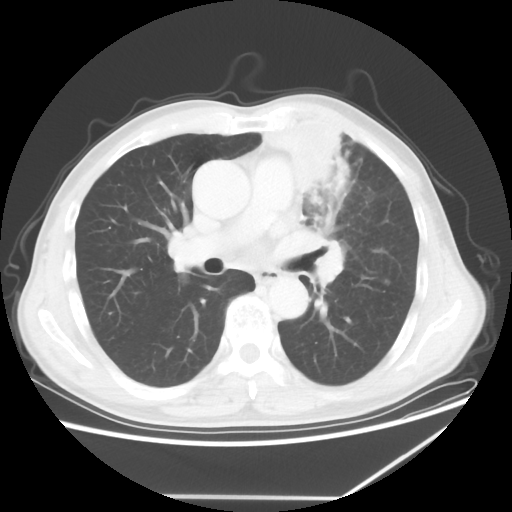
Chest CT, one axial slice; slice 35 of 64 in the series (ordered by position); lung window (W 1500 / L -600 HU); 5 mm slice thickness; 512 × 512 image matrix, field of view 383 × 383 mm. Male patient, age 64 years. Case-level facts recorded for this patient, not image findings: clinical TNM (as recorded): T1c N1 M1; histopathological grade: G2.
Structures marked on this image (bounding box drawn by a radiologist):
- lung tumour (recorded histology: squamous cell carcinoma): bounding box (x1, y1, x2, y2) in pixels: (263, 112, 366, 226)